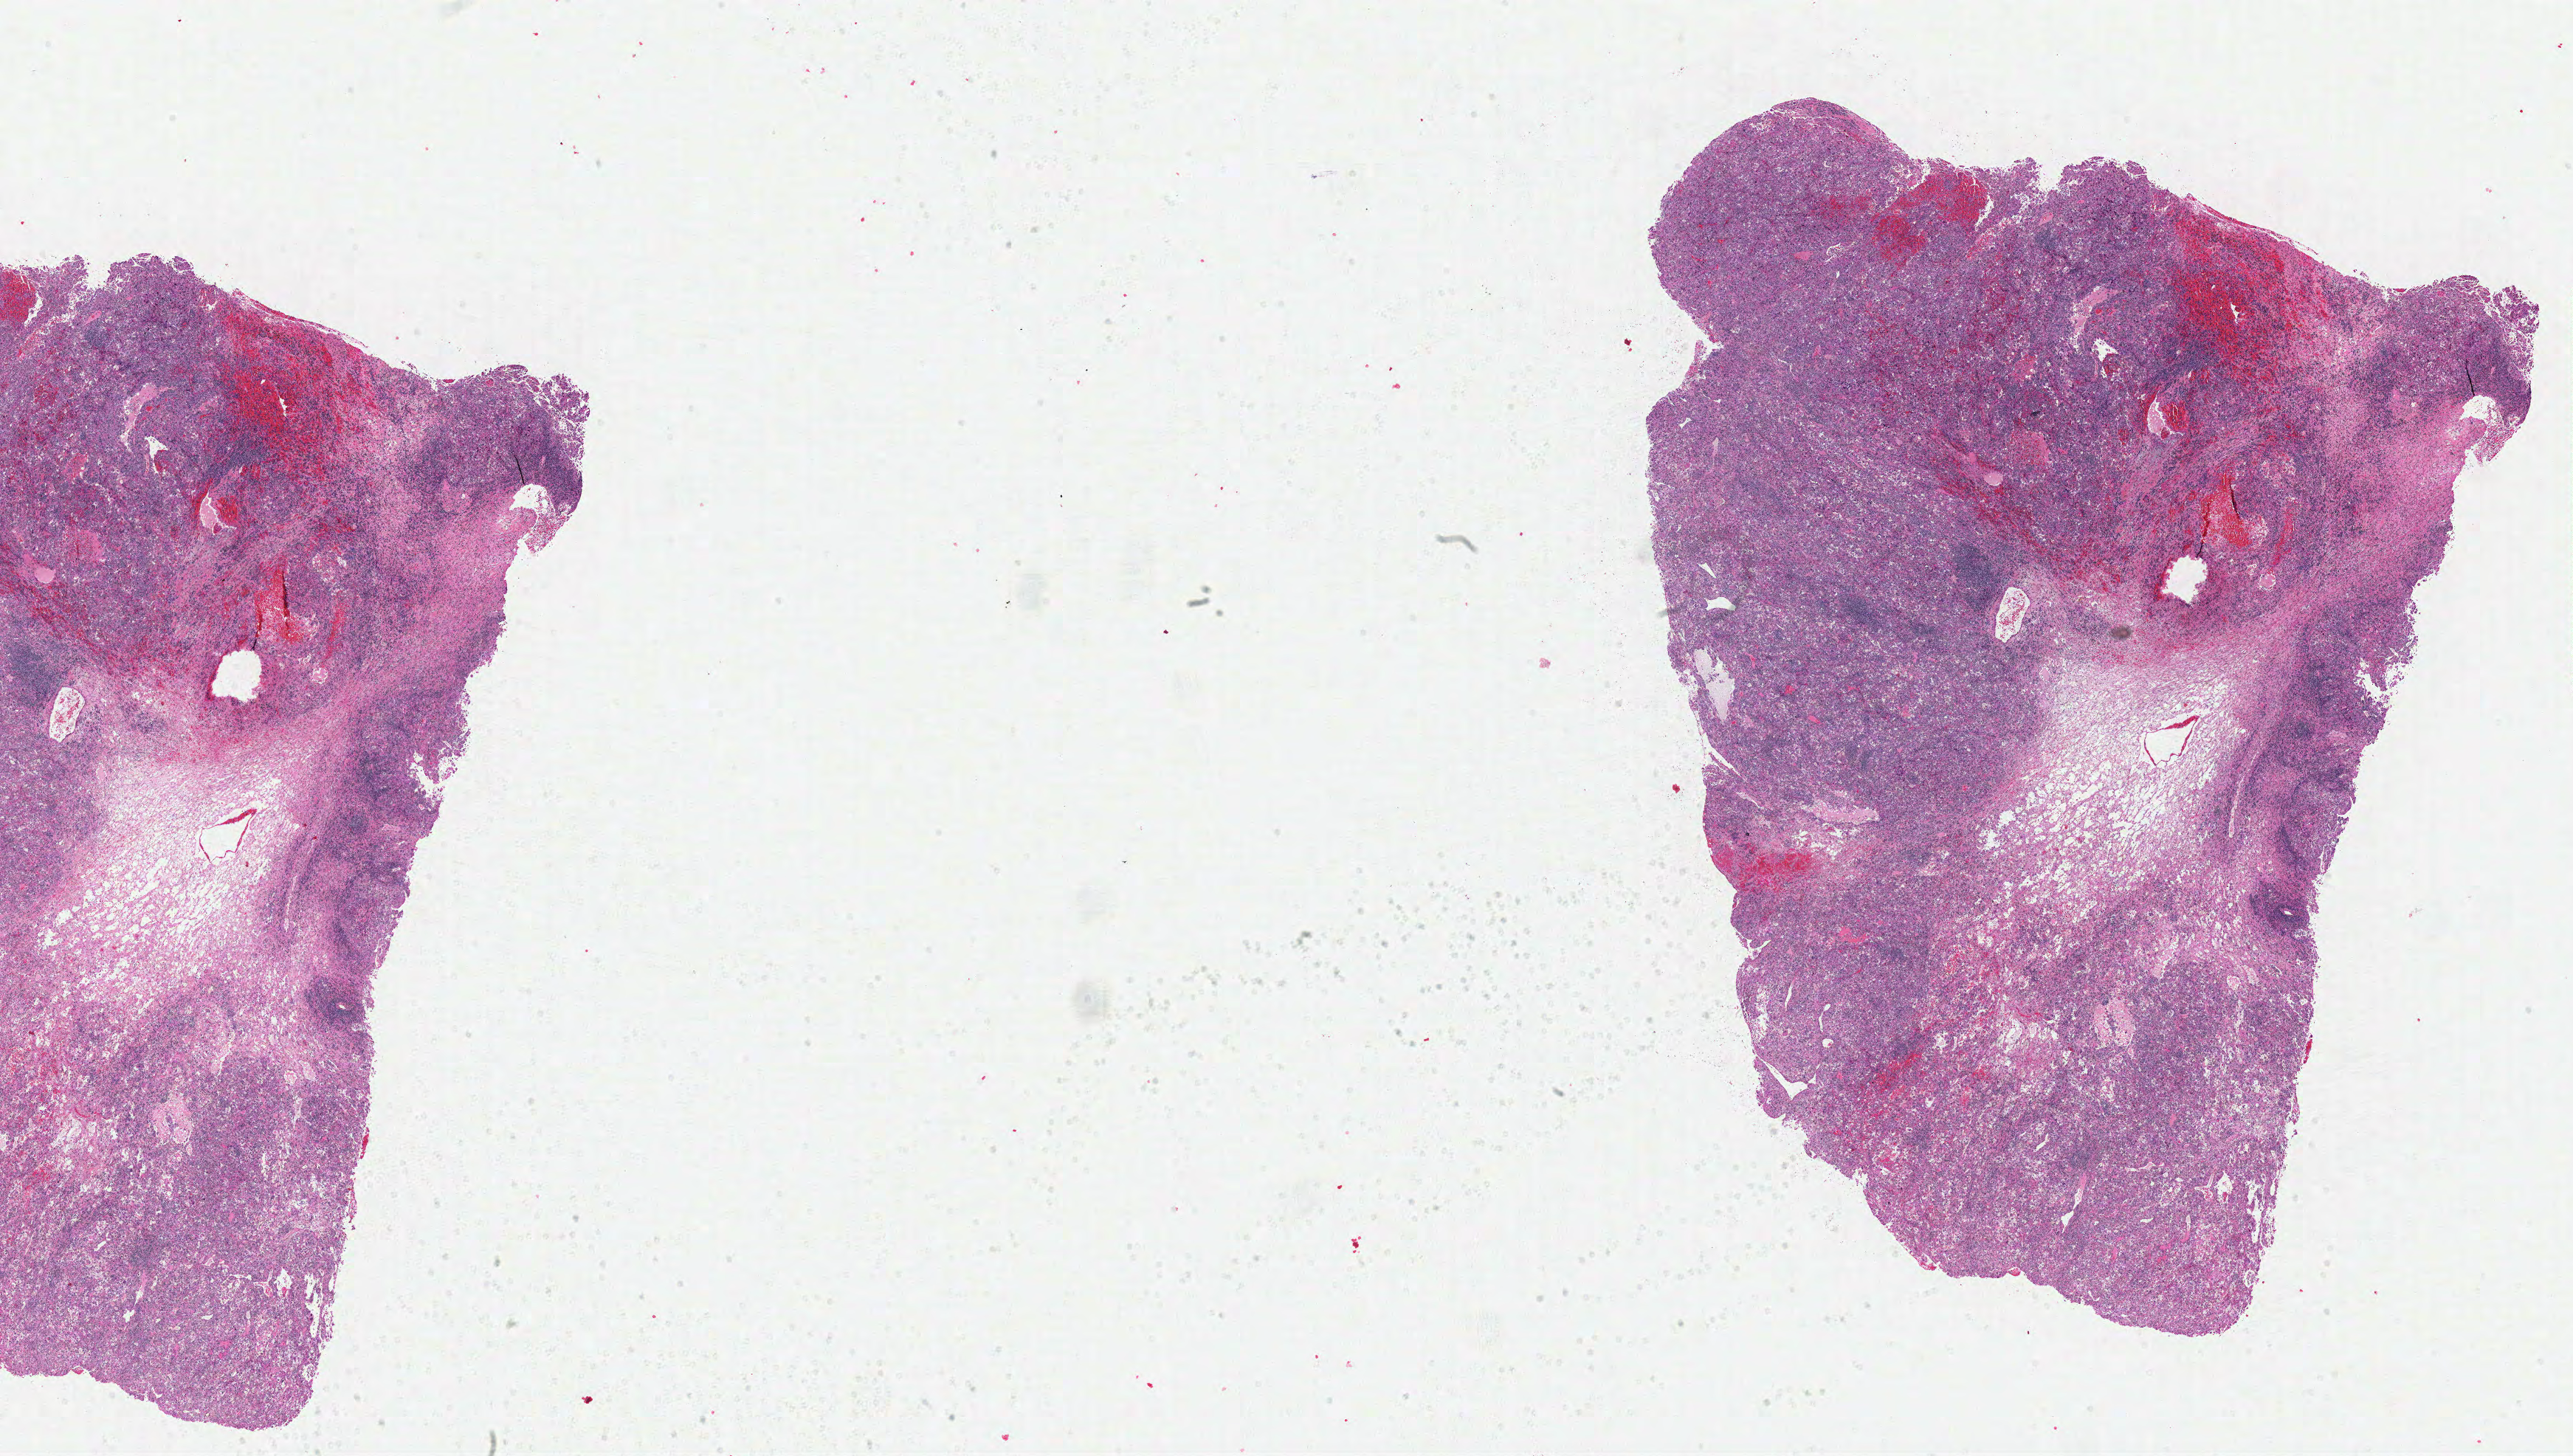
Whole-slide histology image, H&E, whole scanned area (about 27.4 x 15.5 mm, slide scanned at 40x) shown as a low-resolution overview. Formalin-fixed paraffin-embedded (FFPE) diagnostic section. Kidney, primary tumour sample. Female patient; age at initial diagnosis 65 years. Histologic grade: G3 (poorly differentiated).
* diagnosis: Clear cell adenocarcinoma, NOS
* TNM: T1b N0 M0
* AJCC pathologic stage: I
* laterality: right